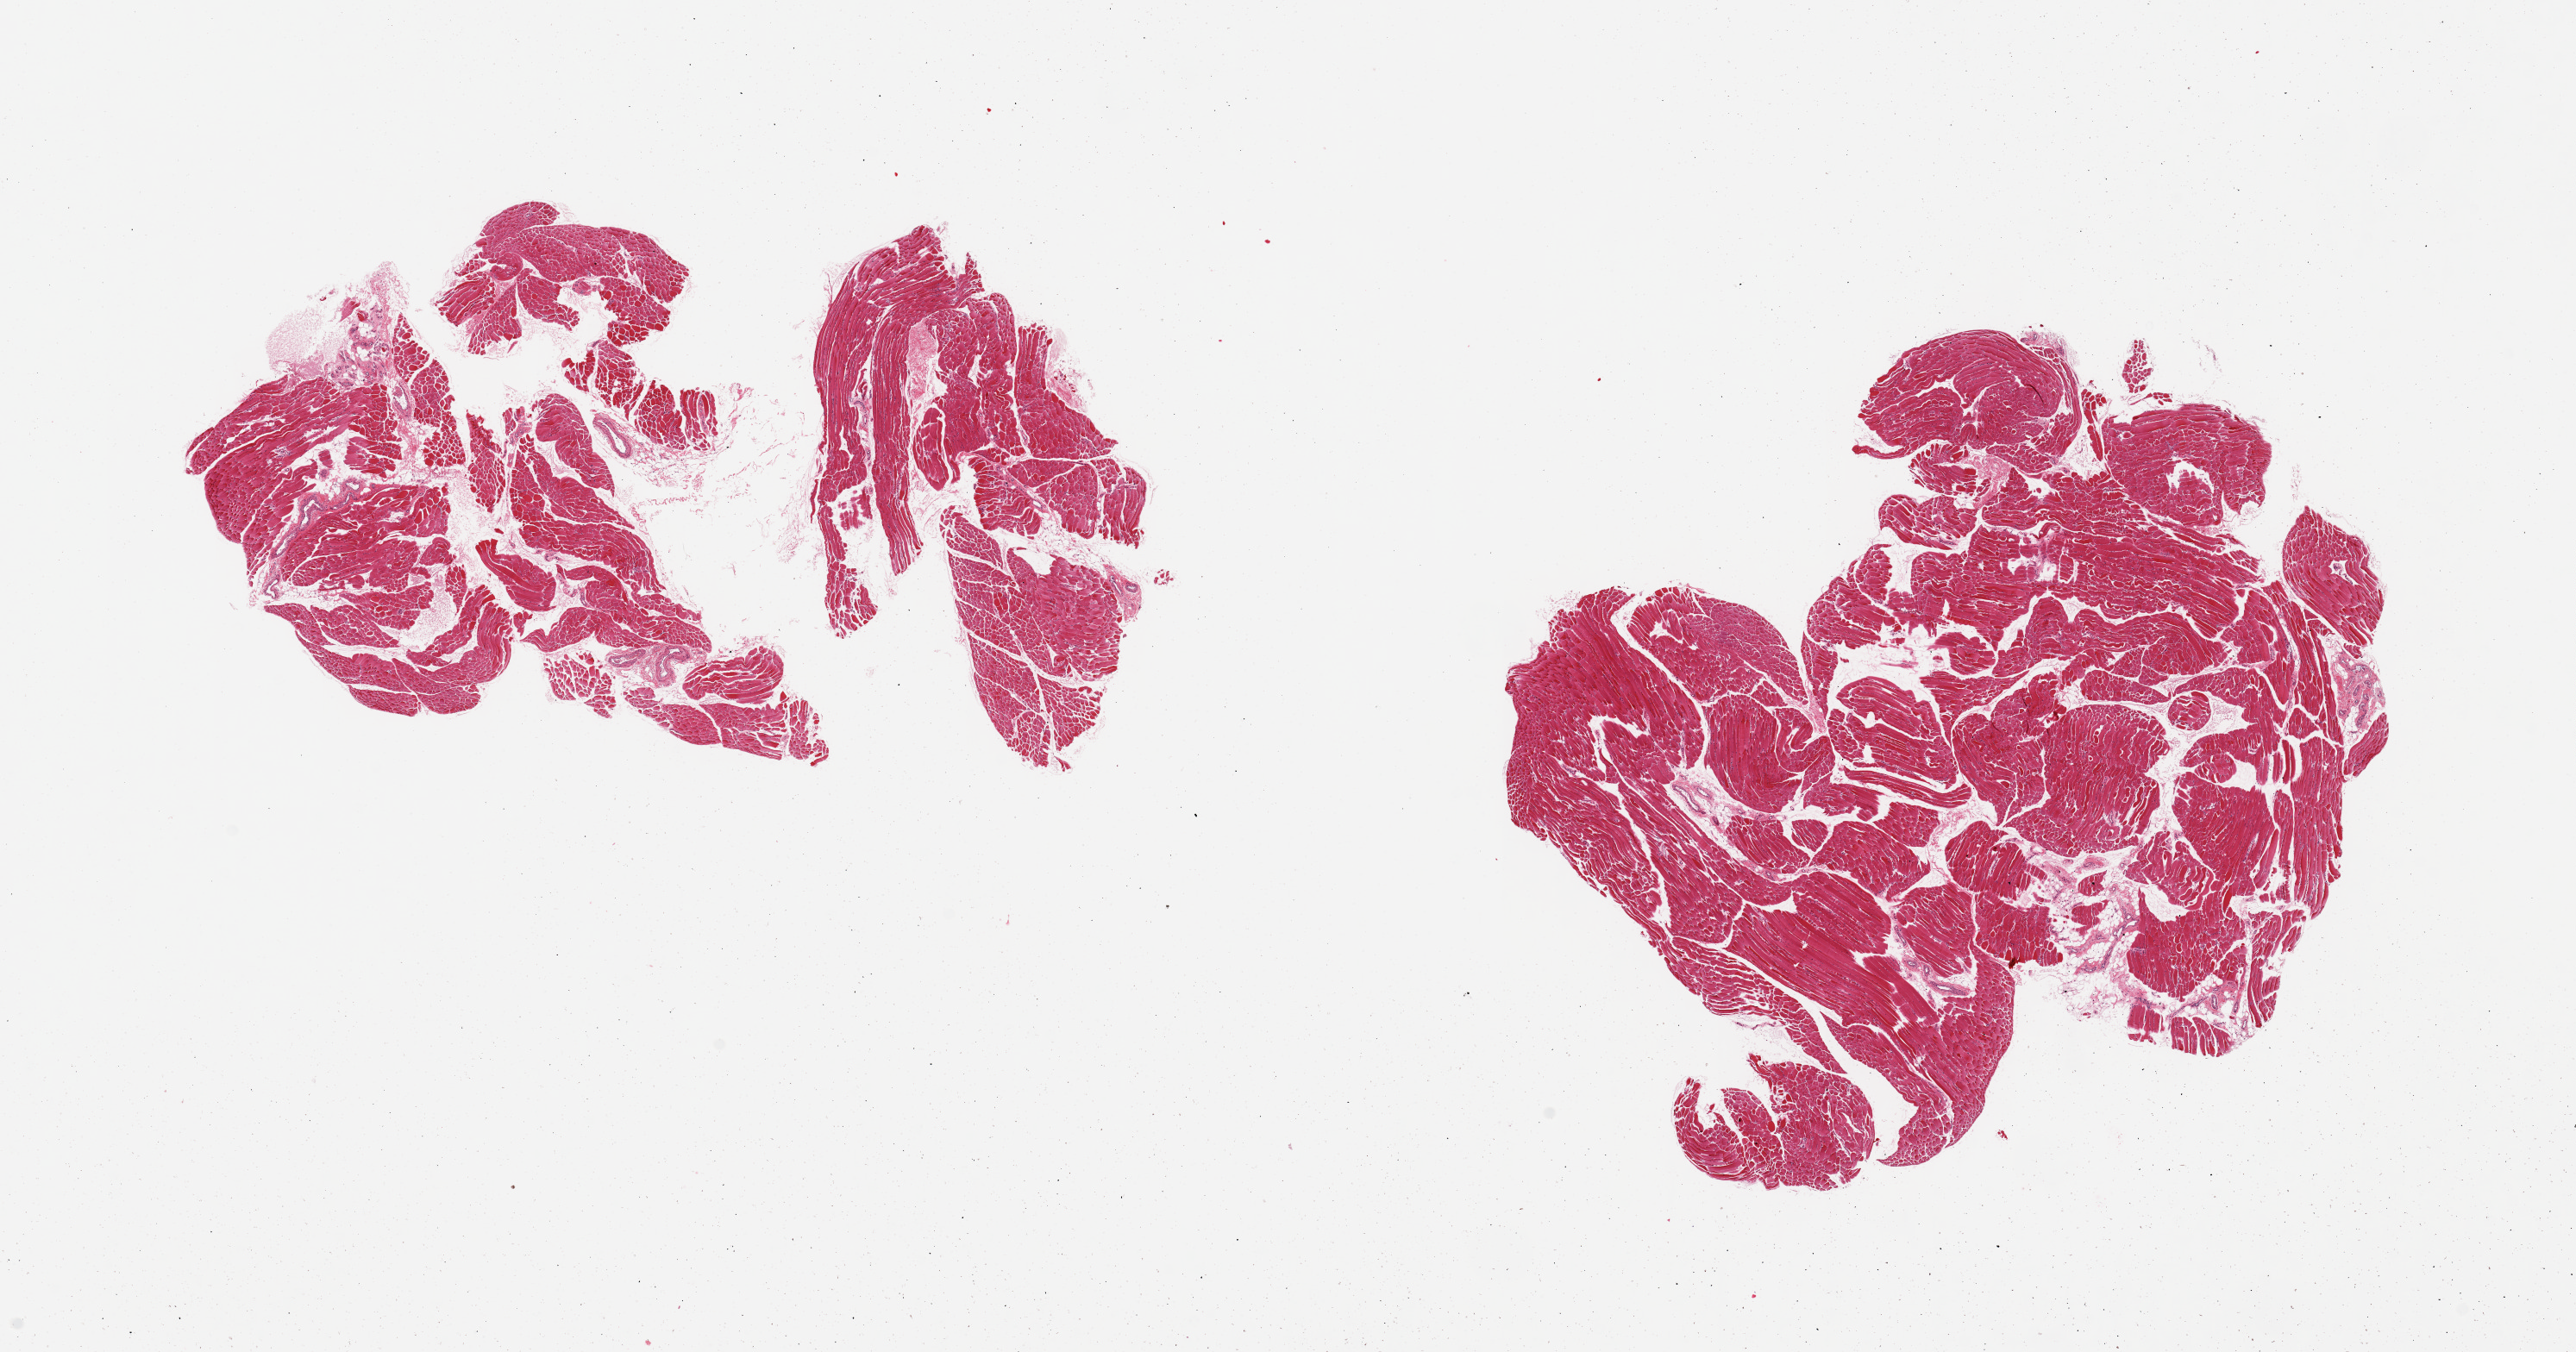
Digitized haematoxylin and eosin-stained section, low-resolution overview of the scanned area, about 23.6 x 12.4 mm (acquisition: 20x scan), PAXgene-fixed paraffin-embedded (PFPE) section, sampled site (target tissue): skeletal muscle, tissue donor sample. Donor: male.
Review note (as recorded): 2 pieces.